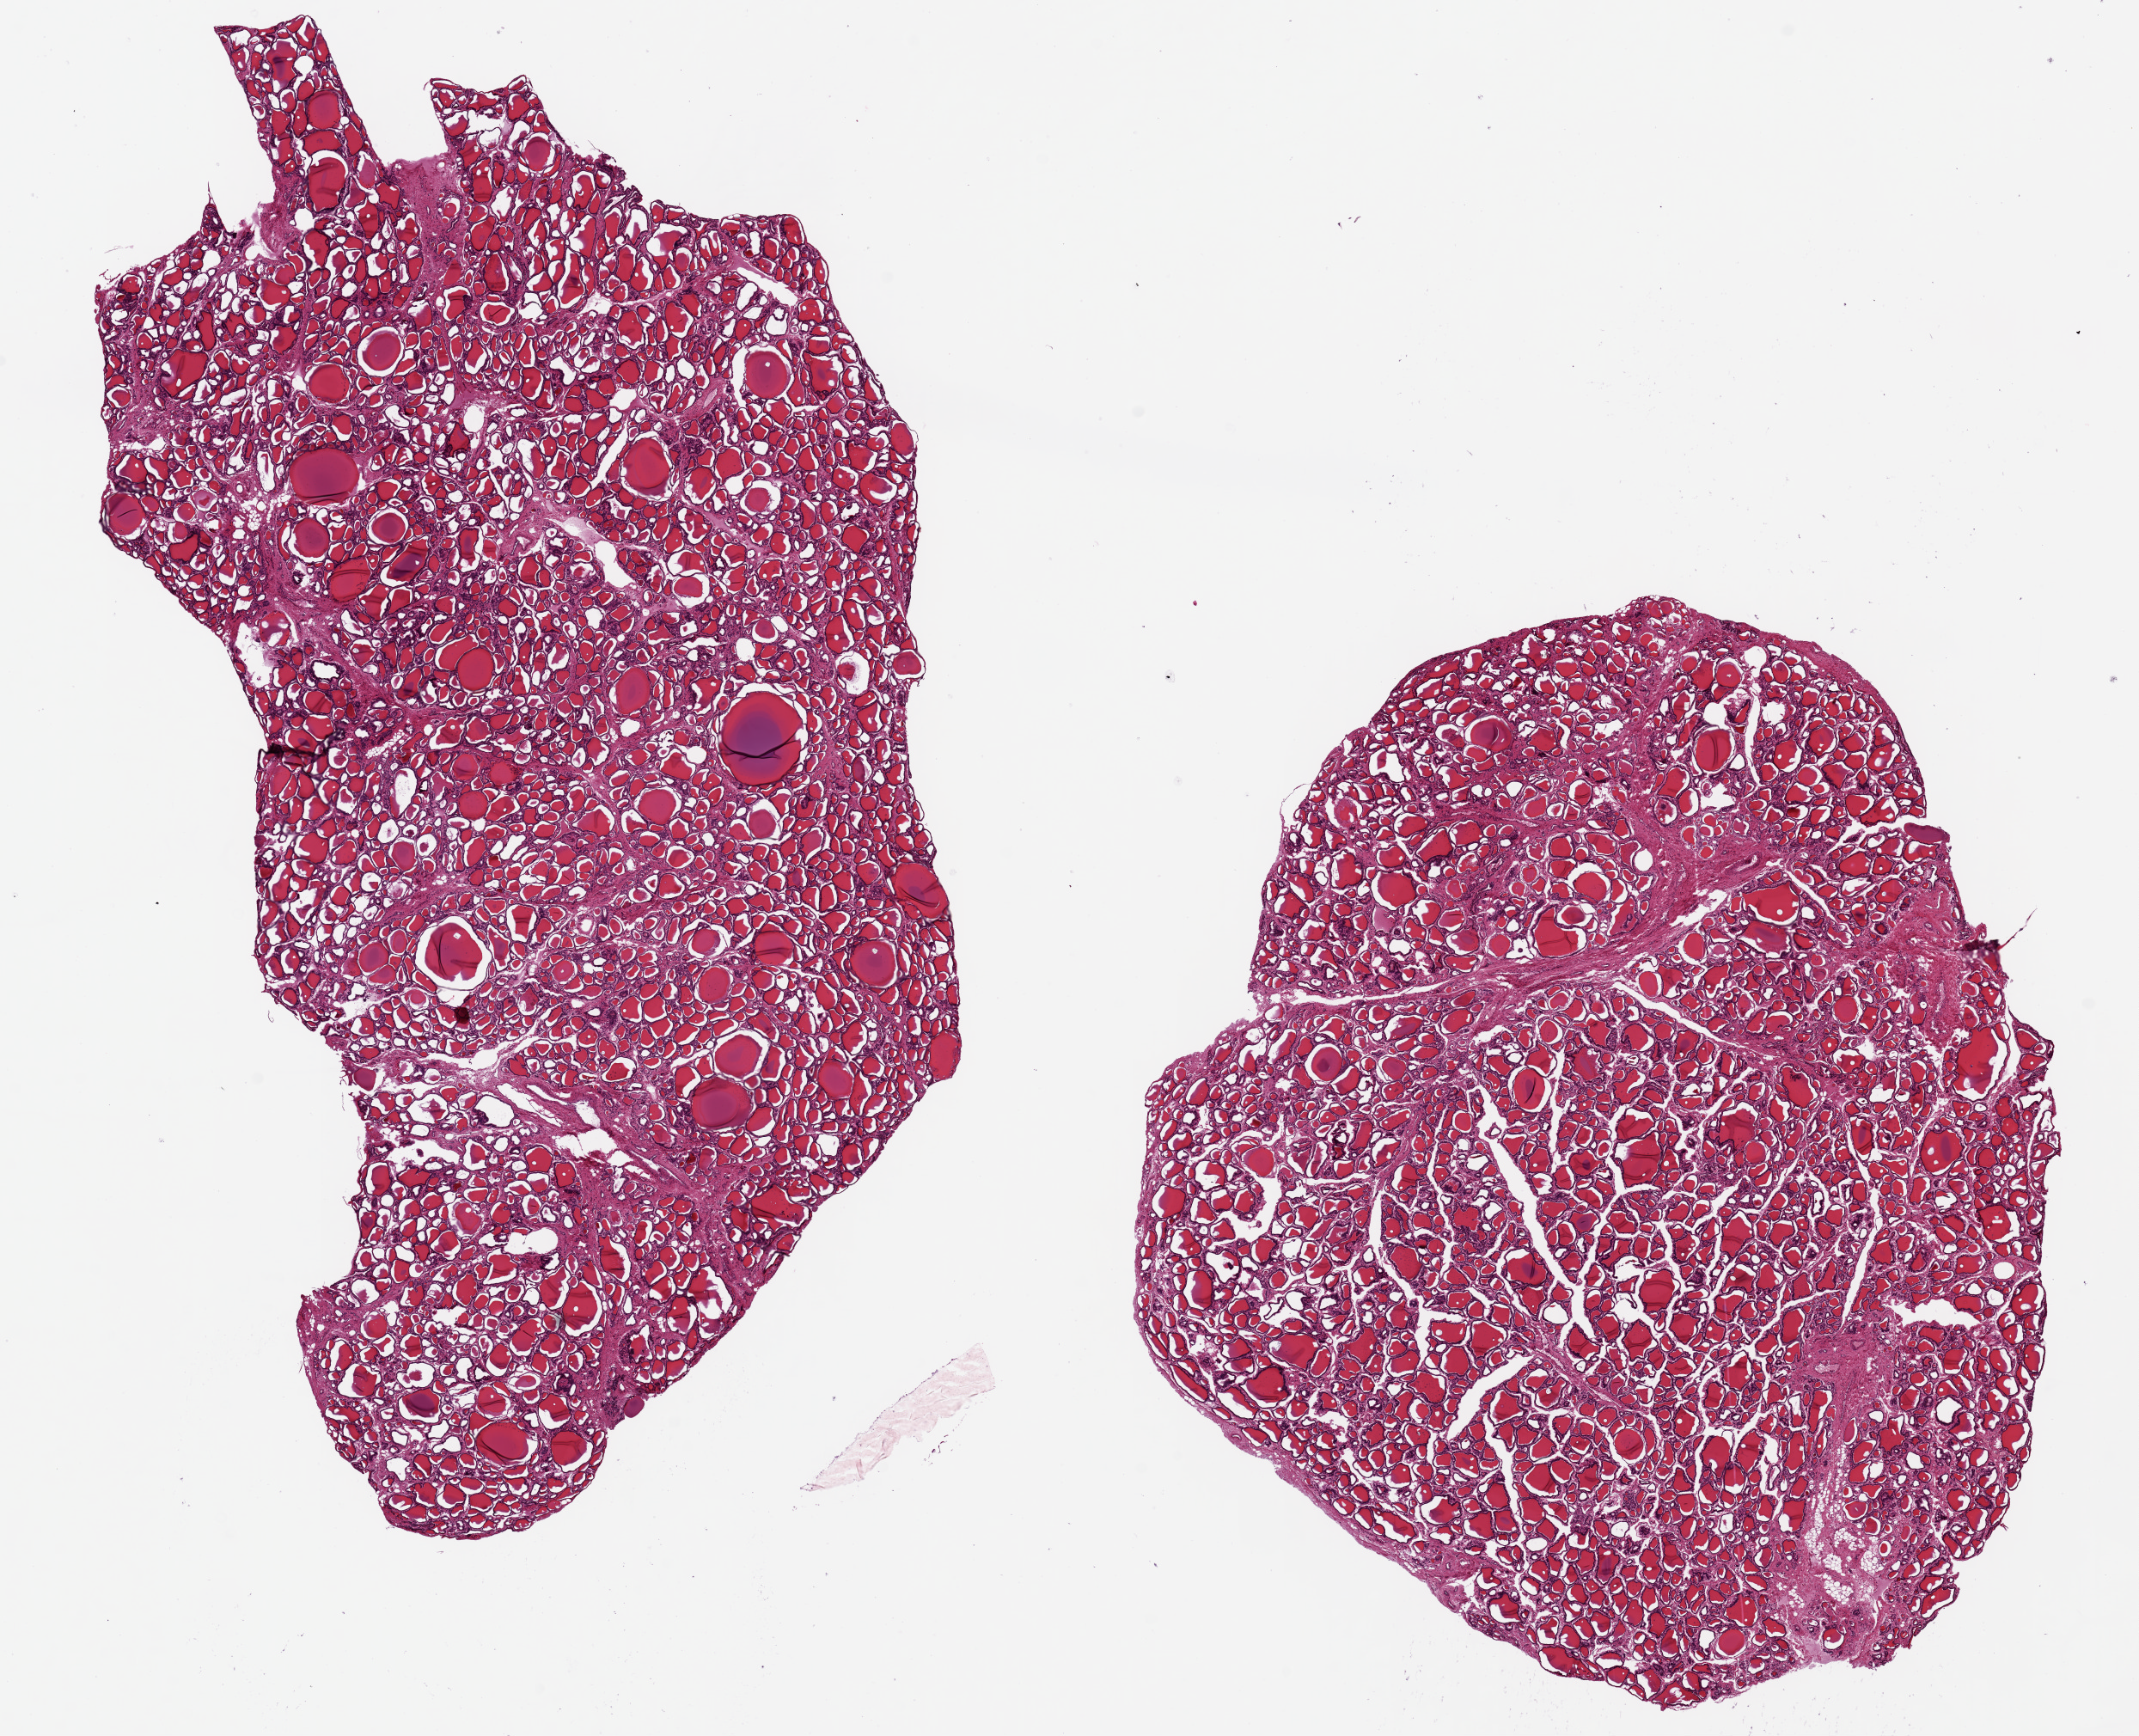
Digitized H&E-stained section, brightfield — whole scanned area (about 19.7 x 16.0 mm, acquisition: 20x scan) shown as a low-resolution overview, PAXgene-fixed paraffin-embedded (PFPE) section, section of thyroid (target tissue), donor tissue sample. Donor: female.
Reviewer comment on this tissue sample: 2 pieces, 14x7.5 & 10x9mm; good specimen.